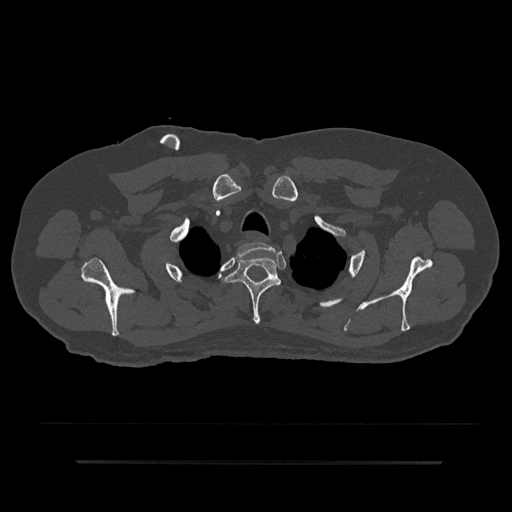
CT including the spine, one axial slice. Slice 701 of 797 in the series (ordered by position). Reconstruction kernel Br40s/3. Bone window (W 1800 / L 400 HU). 512 × 512 image matrix, field of view 464 × 464 mm. Patient: male, 59 years. Case-level facts recorded for this patient, not image findings: primary cancer: bile ducts.
Outlined on this slice (semi-automatic segmentation, software-assisted and operator-edited):
- T1 vertebra: bounding box <238,242,275,258> (left, top, right, bottom; pixels)
- T2 vertebra: <223,255,281,325>